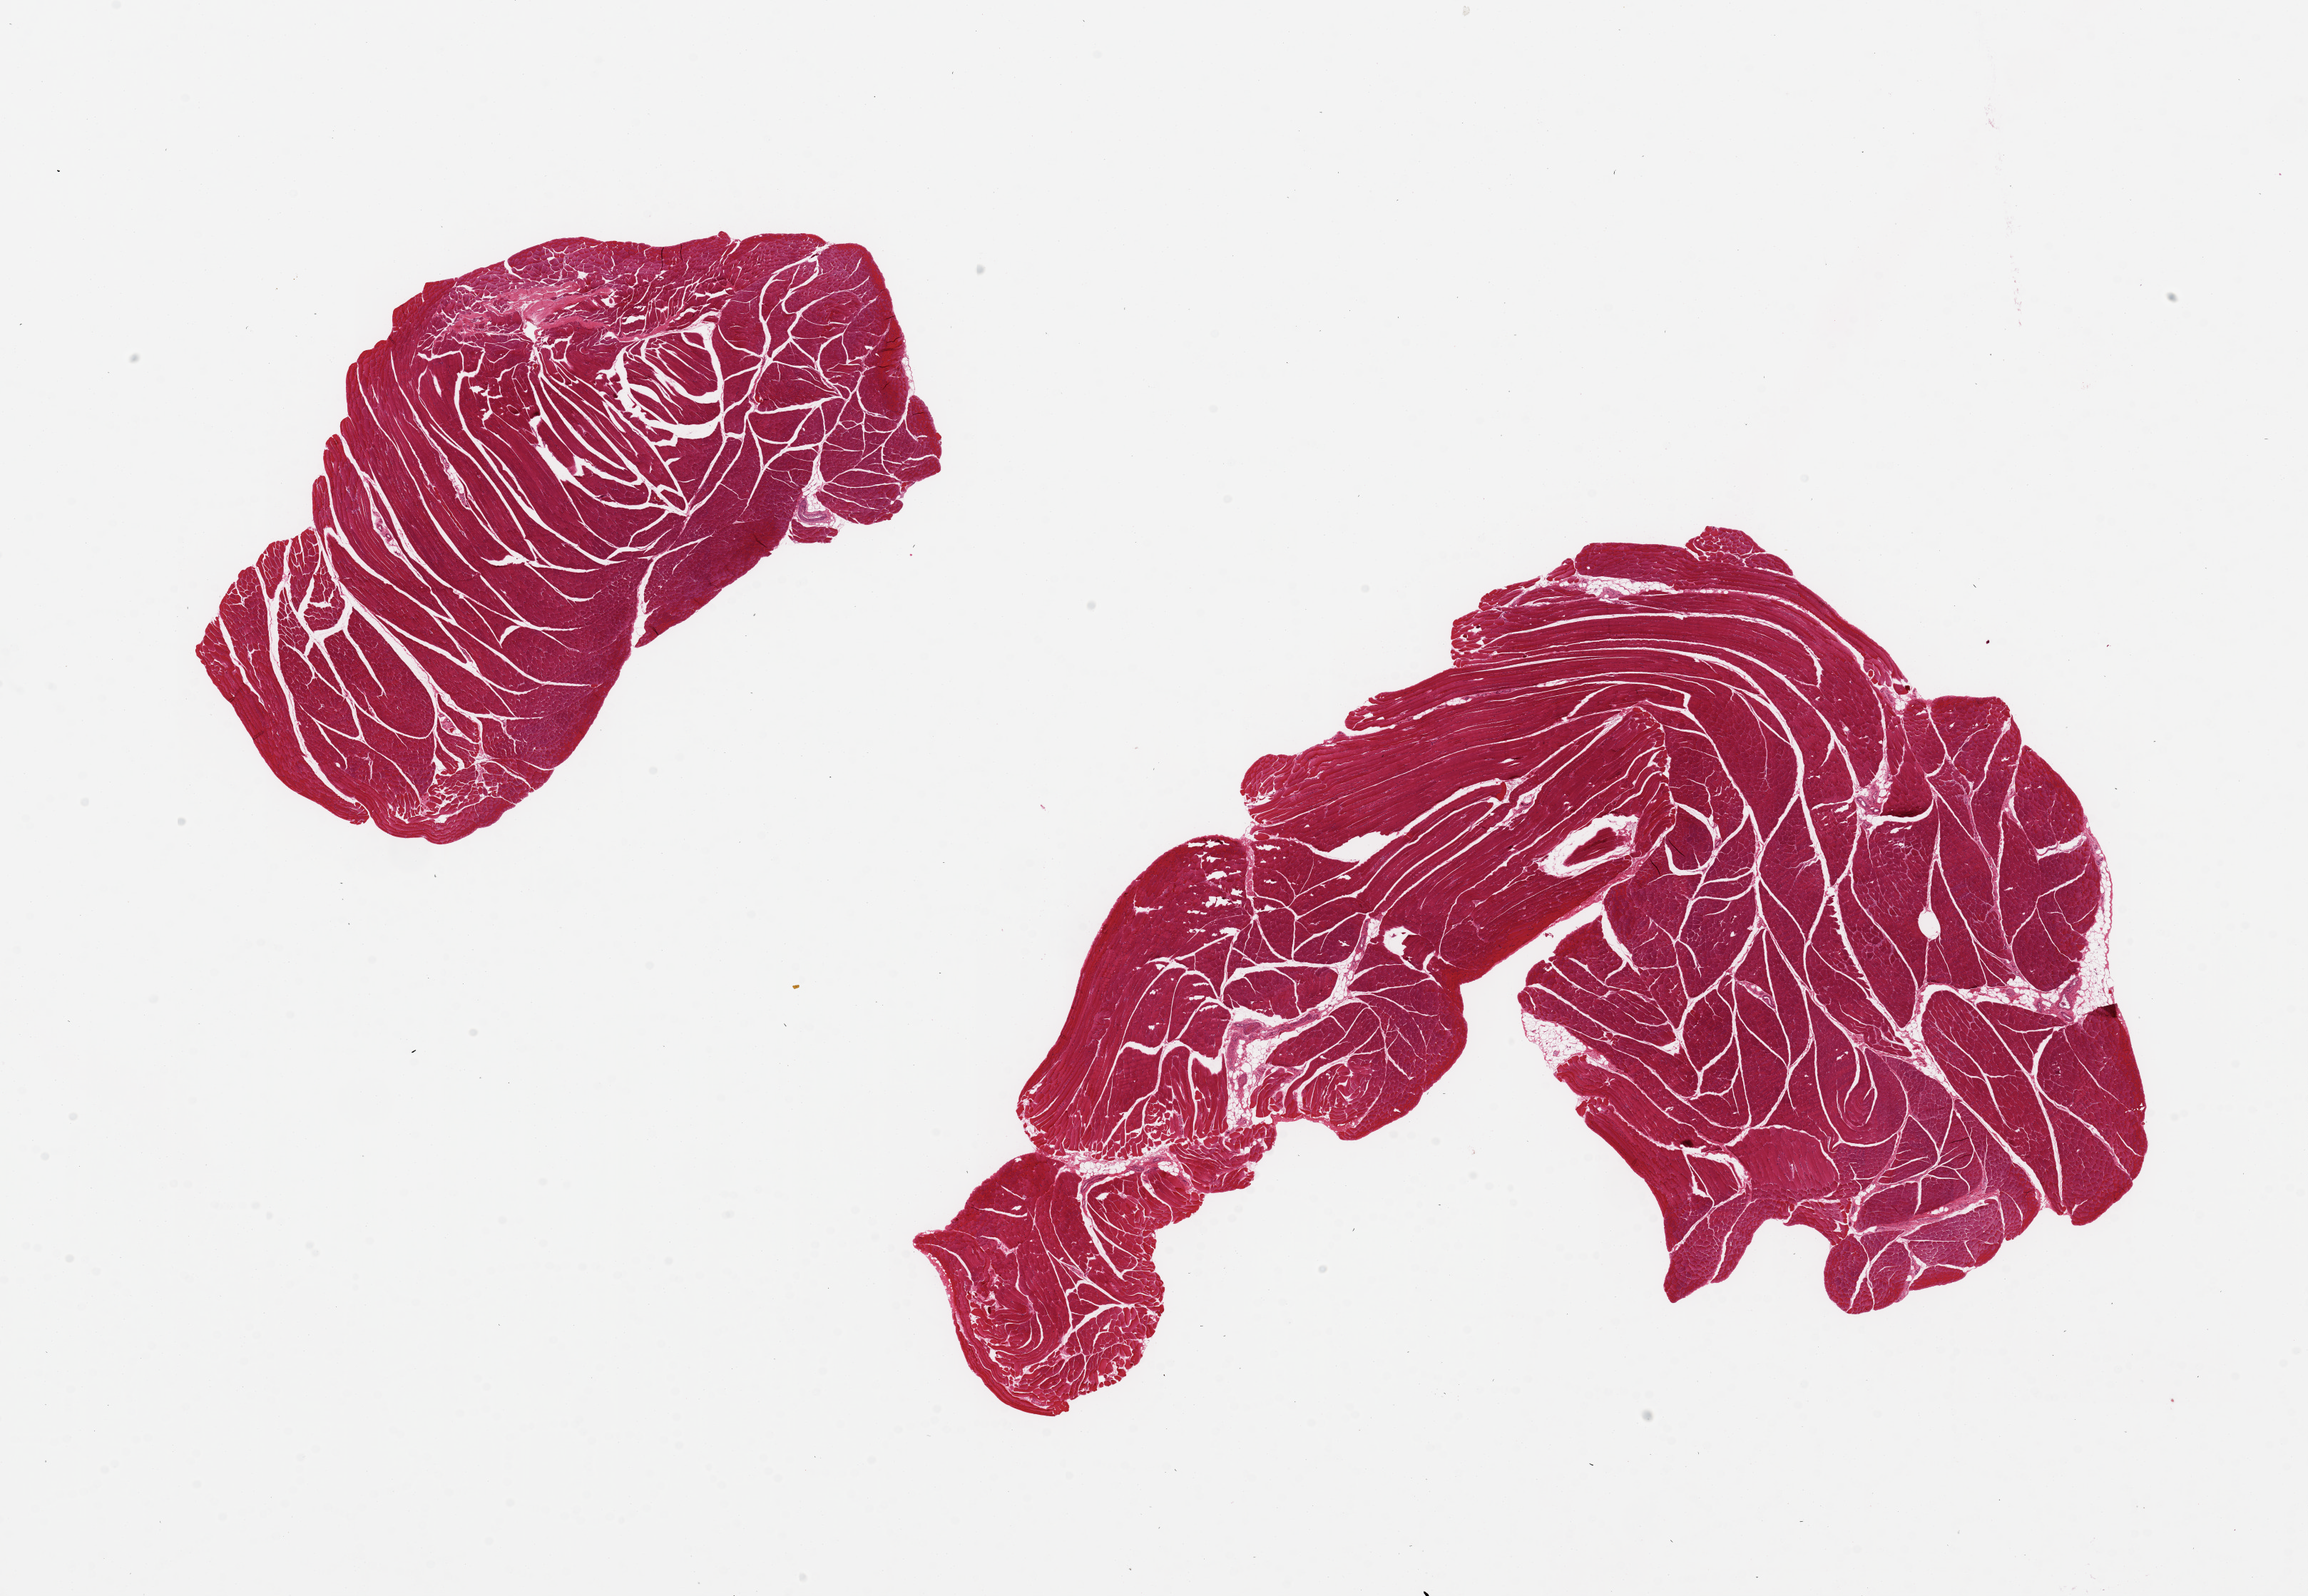
Digitized H&E-stained section, low-resolution overview of the scanned area, about 25.6 x 17.7 mm; PAXgene-fixed paraffin-embedded (PFPE) section; target tissue: skeletal muscle; donor tissue sample. Male donor.
Reviewer comment on this tissue sample: 2 pieces, ~10x6mm, minimal interstitial fat.